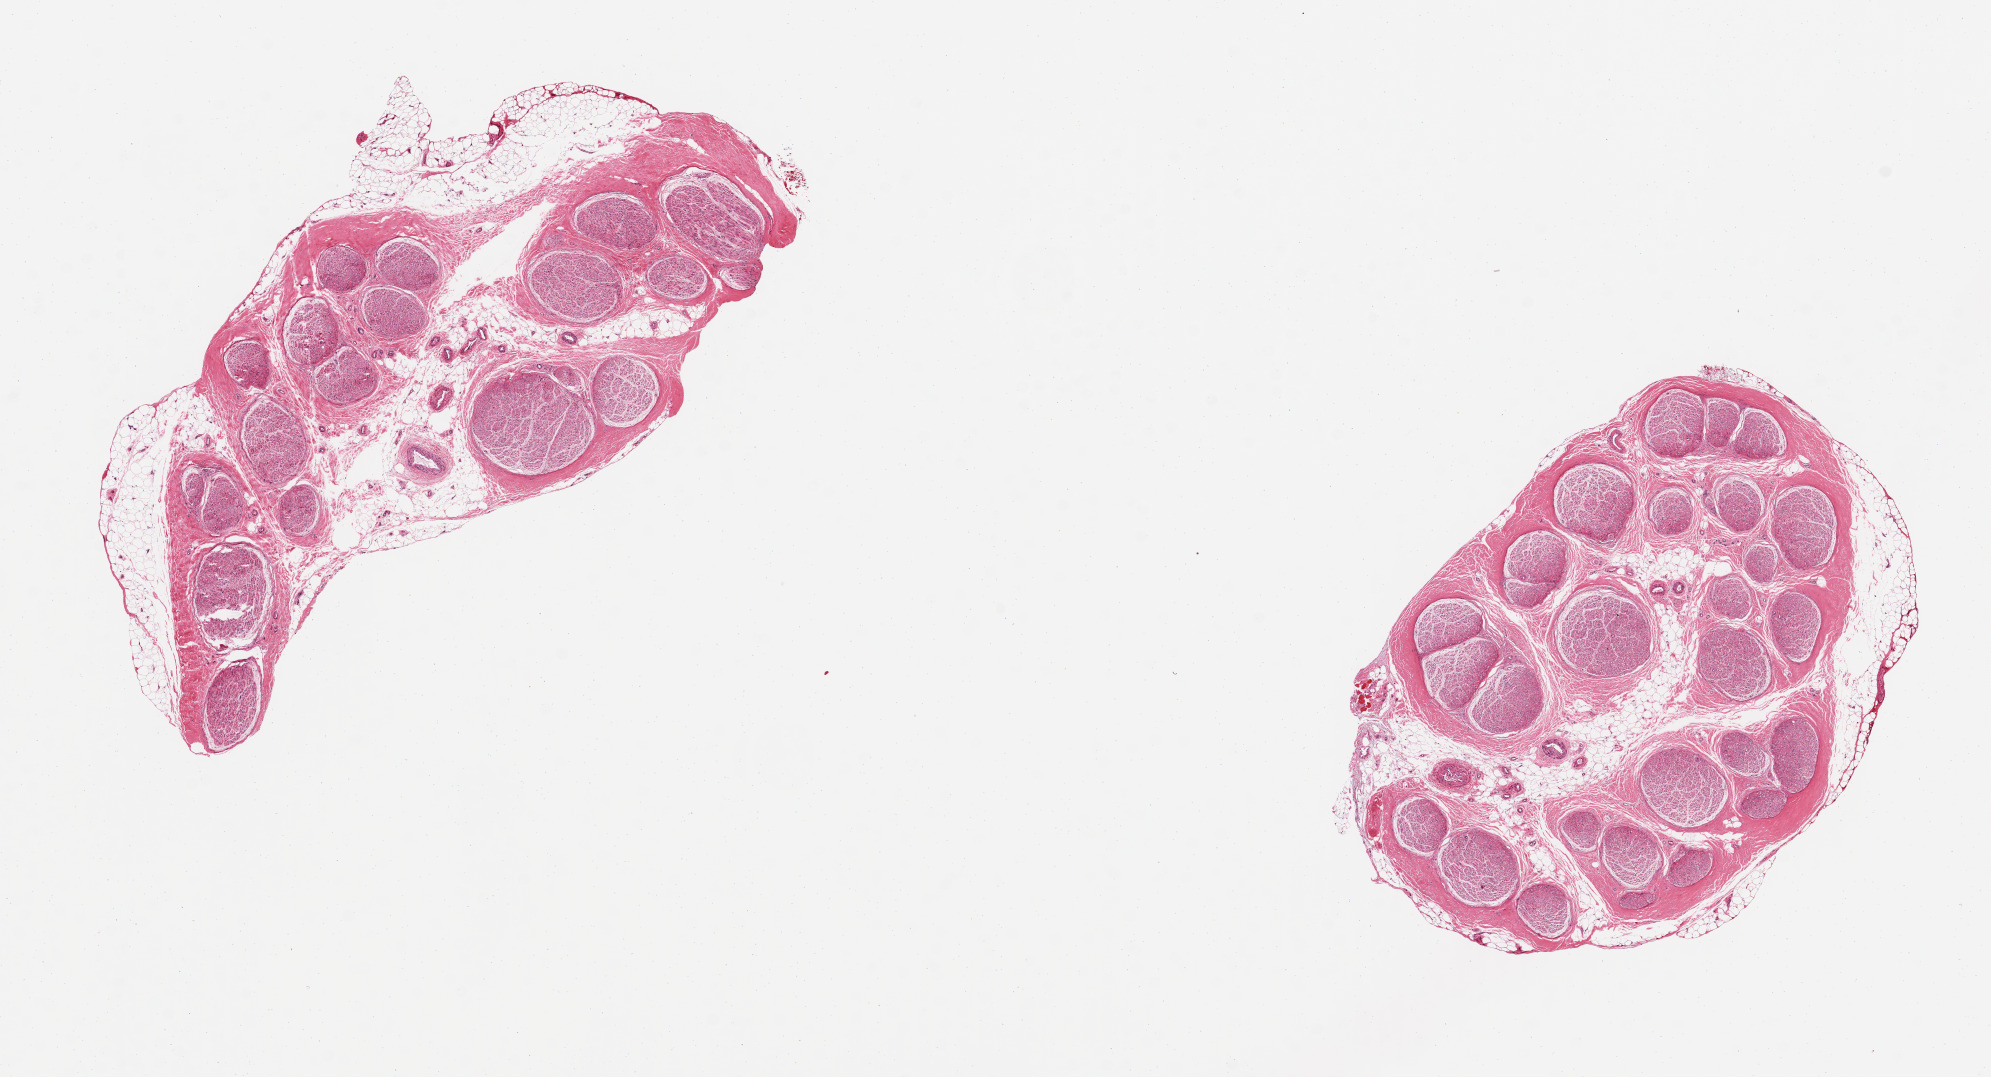
Digitized H&E-stained section, shown as a low-resolution overview of the whole scanned area (about 15.8 x 8.5 mm). PAXgene-fixed, paraffin-embedded tissue. Target tissue: tibial nerve. Donor tissue sample. Donor: male.
Reviewer comment on this tissue sample: 2 pieces, 6x3 & 5x3 mm; ~20% adipose intermixed and at periphery.